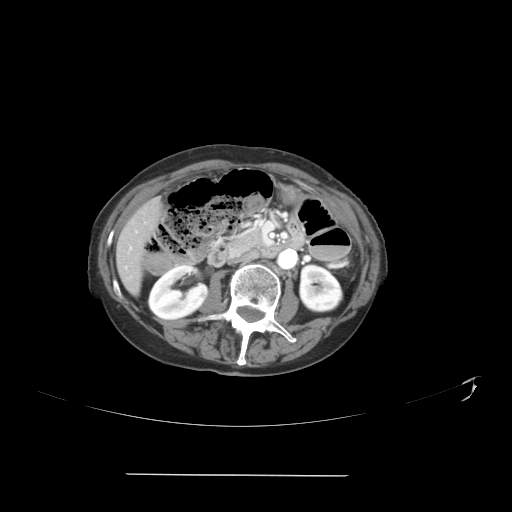
Contrast-enhanced abdominal CT, one axial slice. 120 kVp. Intravenous contrast given. Soft-tissue window (W 400 / L 40 HU). 5 mm slice thickness. 512 × 512 image matrix, field of view 431 × 431 mm. Female patient, age 74 years. From the clinical record (not read from this slice): diagnosis: colorectal cancer liver metastases, imaged before liver resection; multiple liver metastases: yes; largest metastasis: 3.3 cm; disease in both lobes: yes.
Annotated regions visible in this slice (outlined manually by an expert reader):
- hepatic veins: box from (x=125, y=231) to (x=137, y=269) px
- liver: (x=118, y=202)–(x=159, y=290)
- planned liver remnant (the part of the liver to remain after resection): (x=122, y=202)–(x=160, y=243)